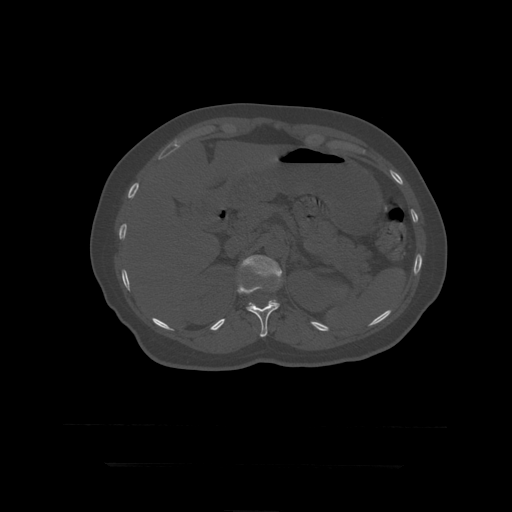
CT including the spine, one axial slice; slice 190 of 399 in the series (ordered by position); reconstruction kernel STANDARD; 120 kVp; bone window (W 1800 / L 400 HU); 512 × 512 image matrix. Patient age 41 years. From the clinical record (not read from this slice): primary cancer: breast.
Outlined on this slice (semi-automatically segmented with operator editing):
- L1 vertebra: bounding box [x1, y1, x2, y2] px = [241, 255, 283, 306]
- T12 vertebra: [237, 284, 280, 337]